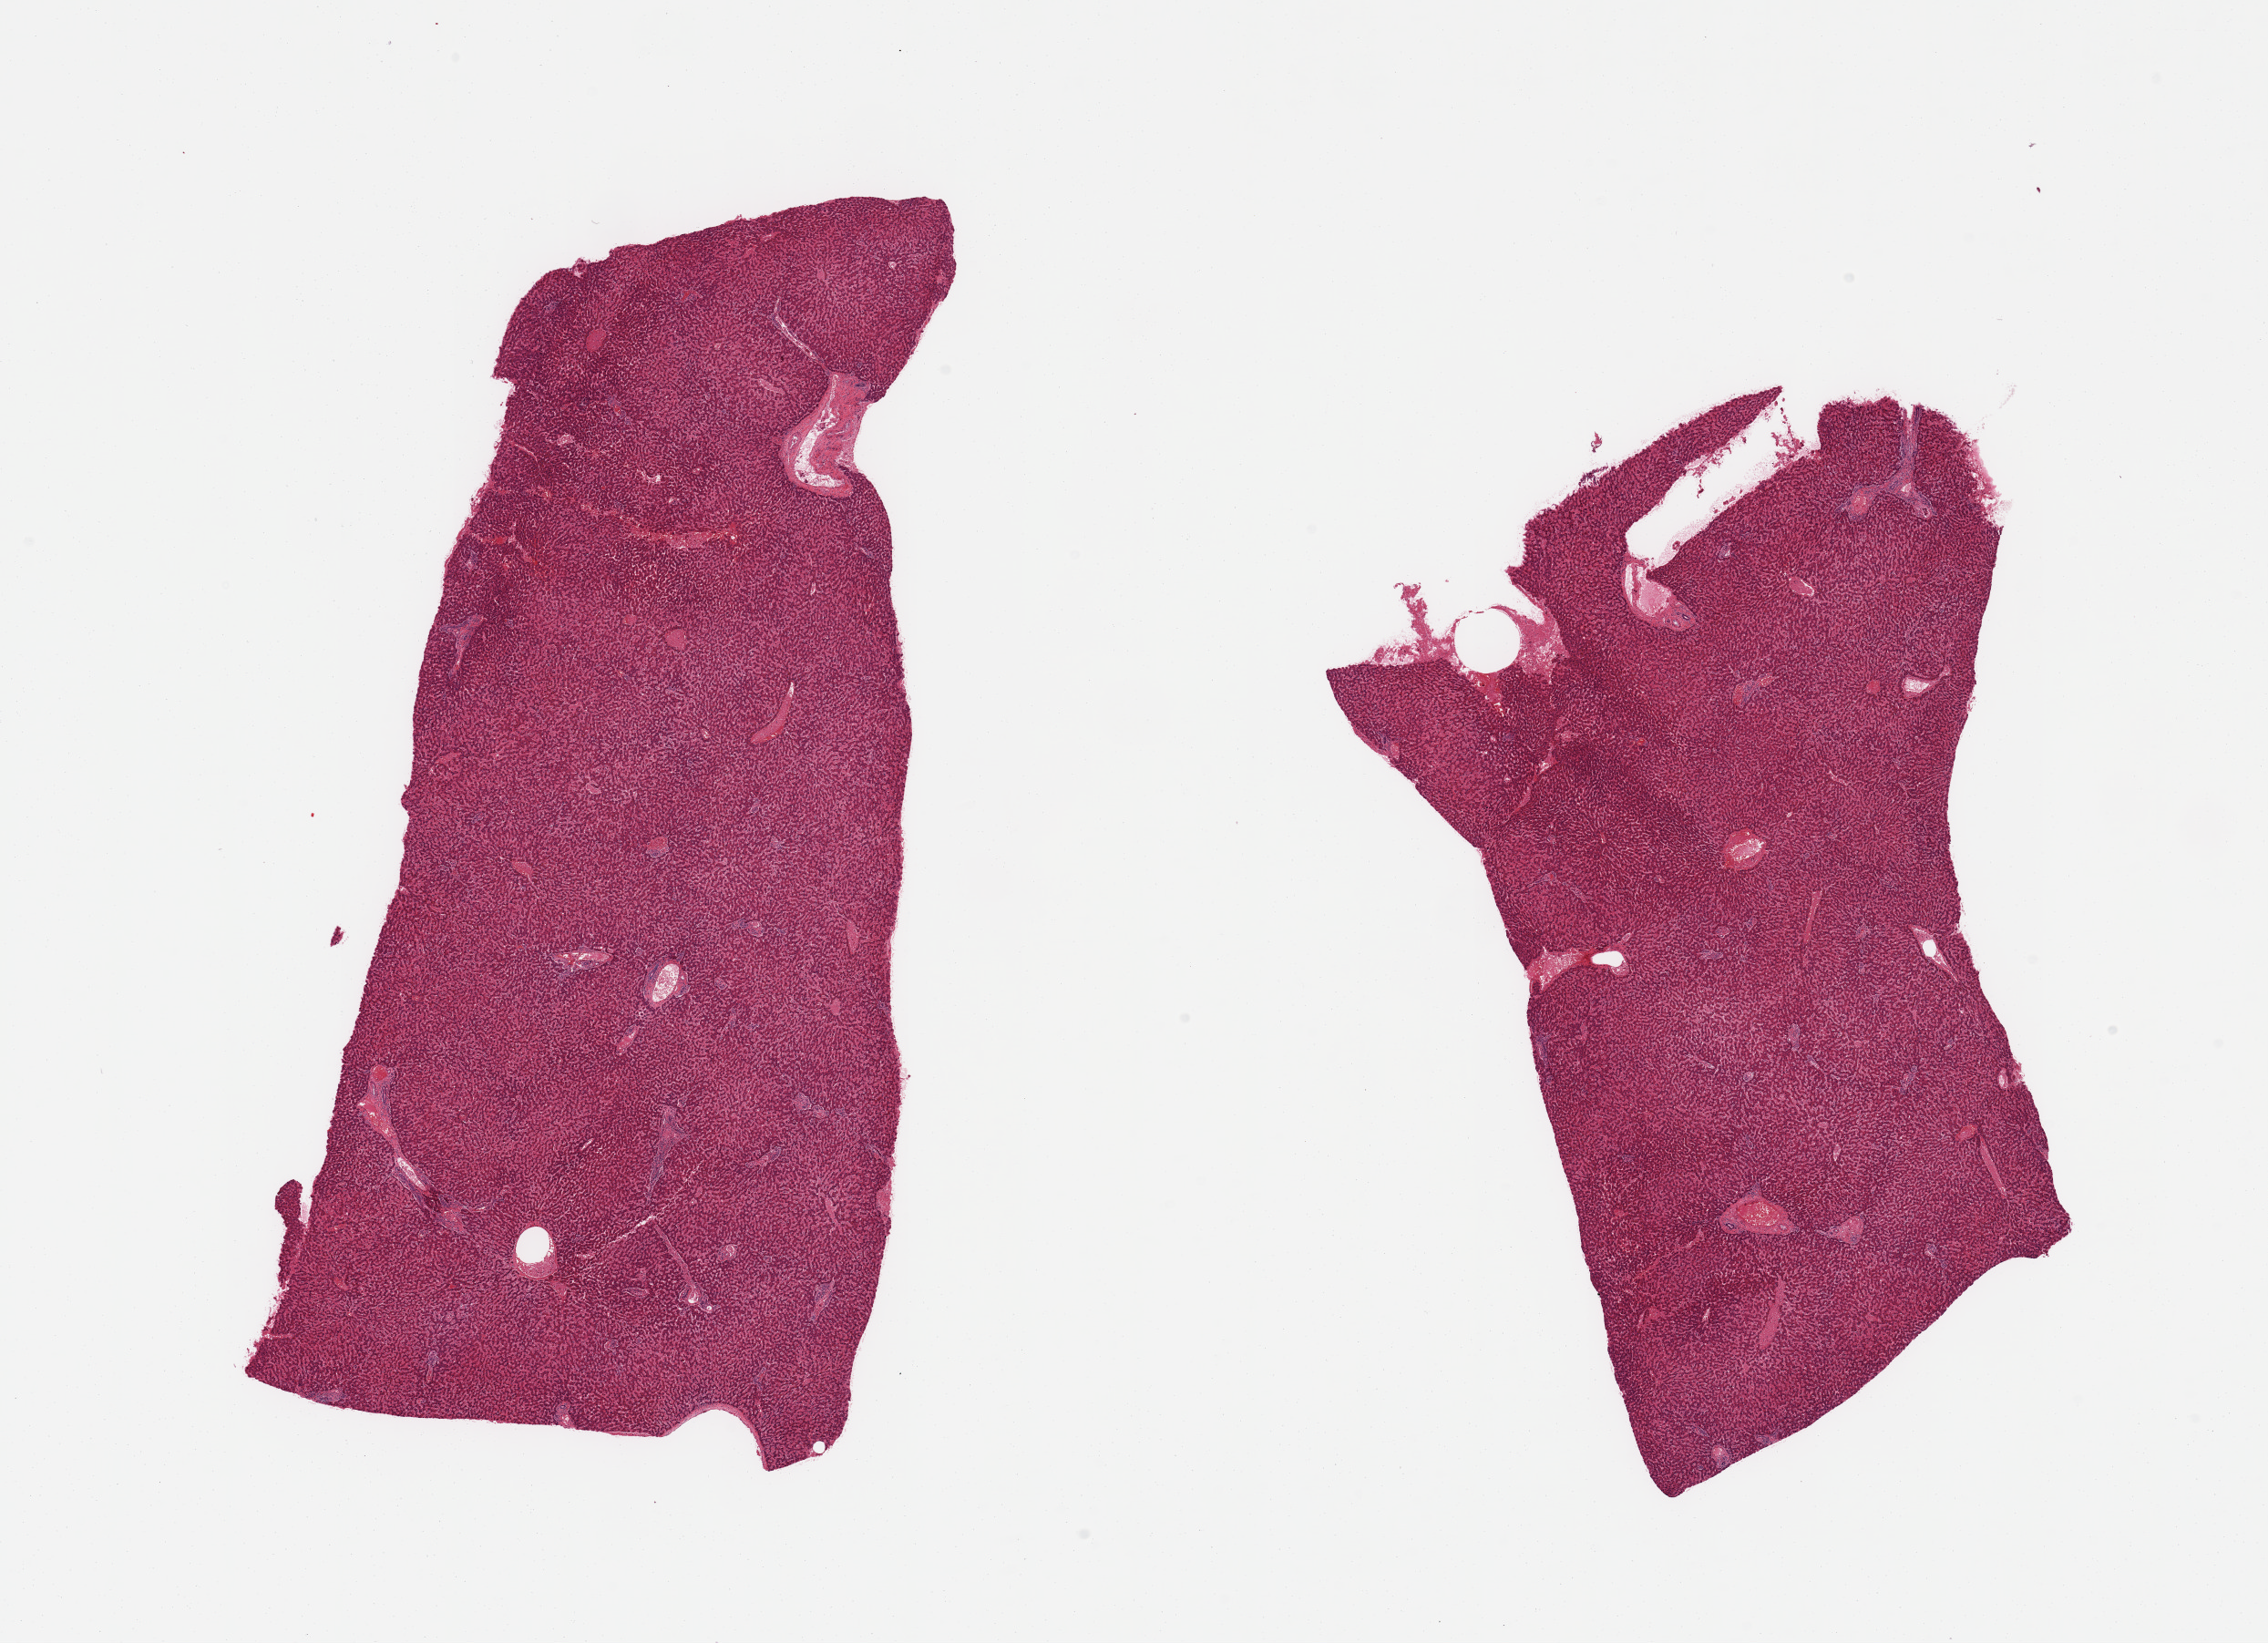
Digitized haematoxylin and eosin-stained section — shown as a low-resolution overview of the whole scanned area (about 19.7 x 14.3 mm, acquisition: 20x scan). PAXgene-fixed paraffin-embedded (PFPE) section. Target tissue: liver. Donor tissue sample. Donor sex: male.
* reviewer comment on this tissue sample: 2 pieces; congested